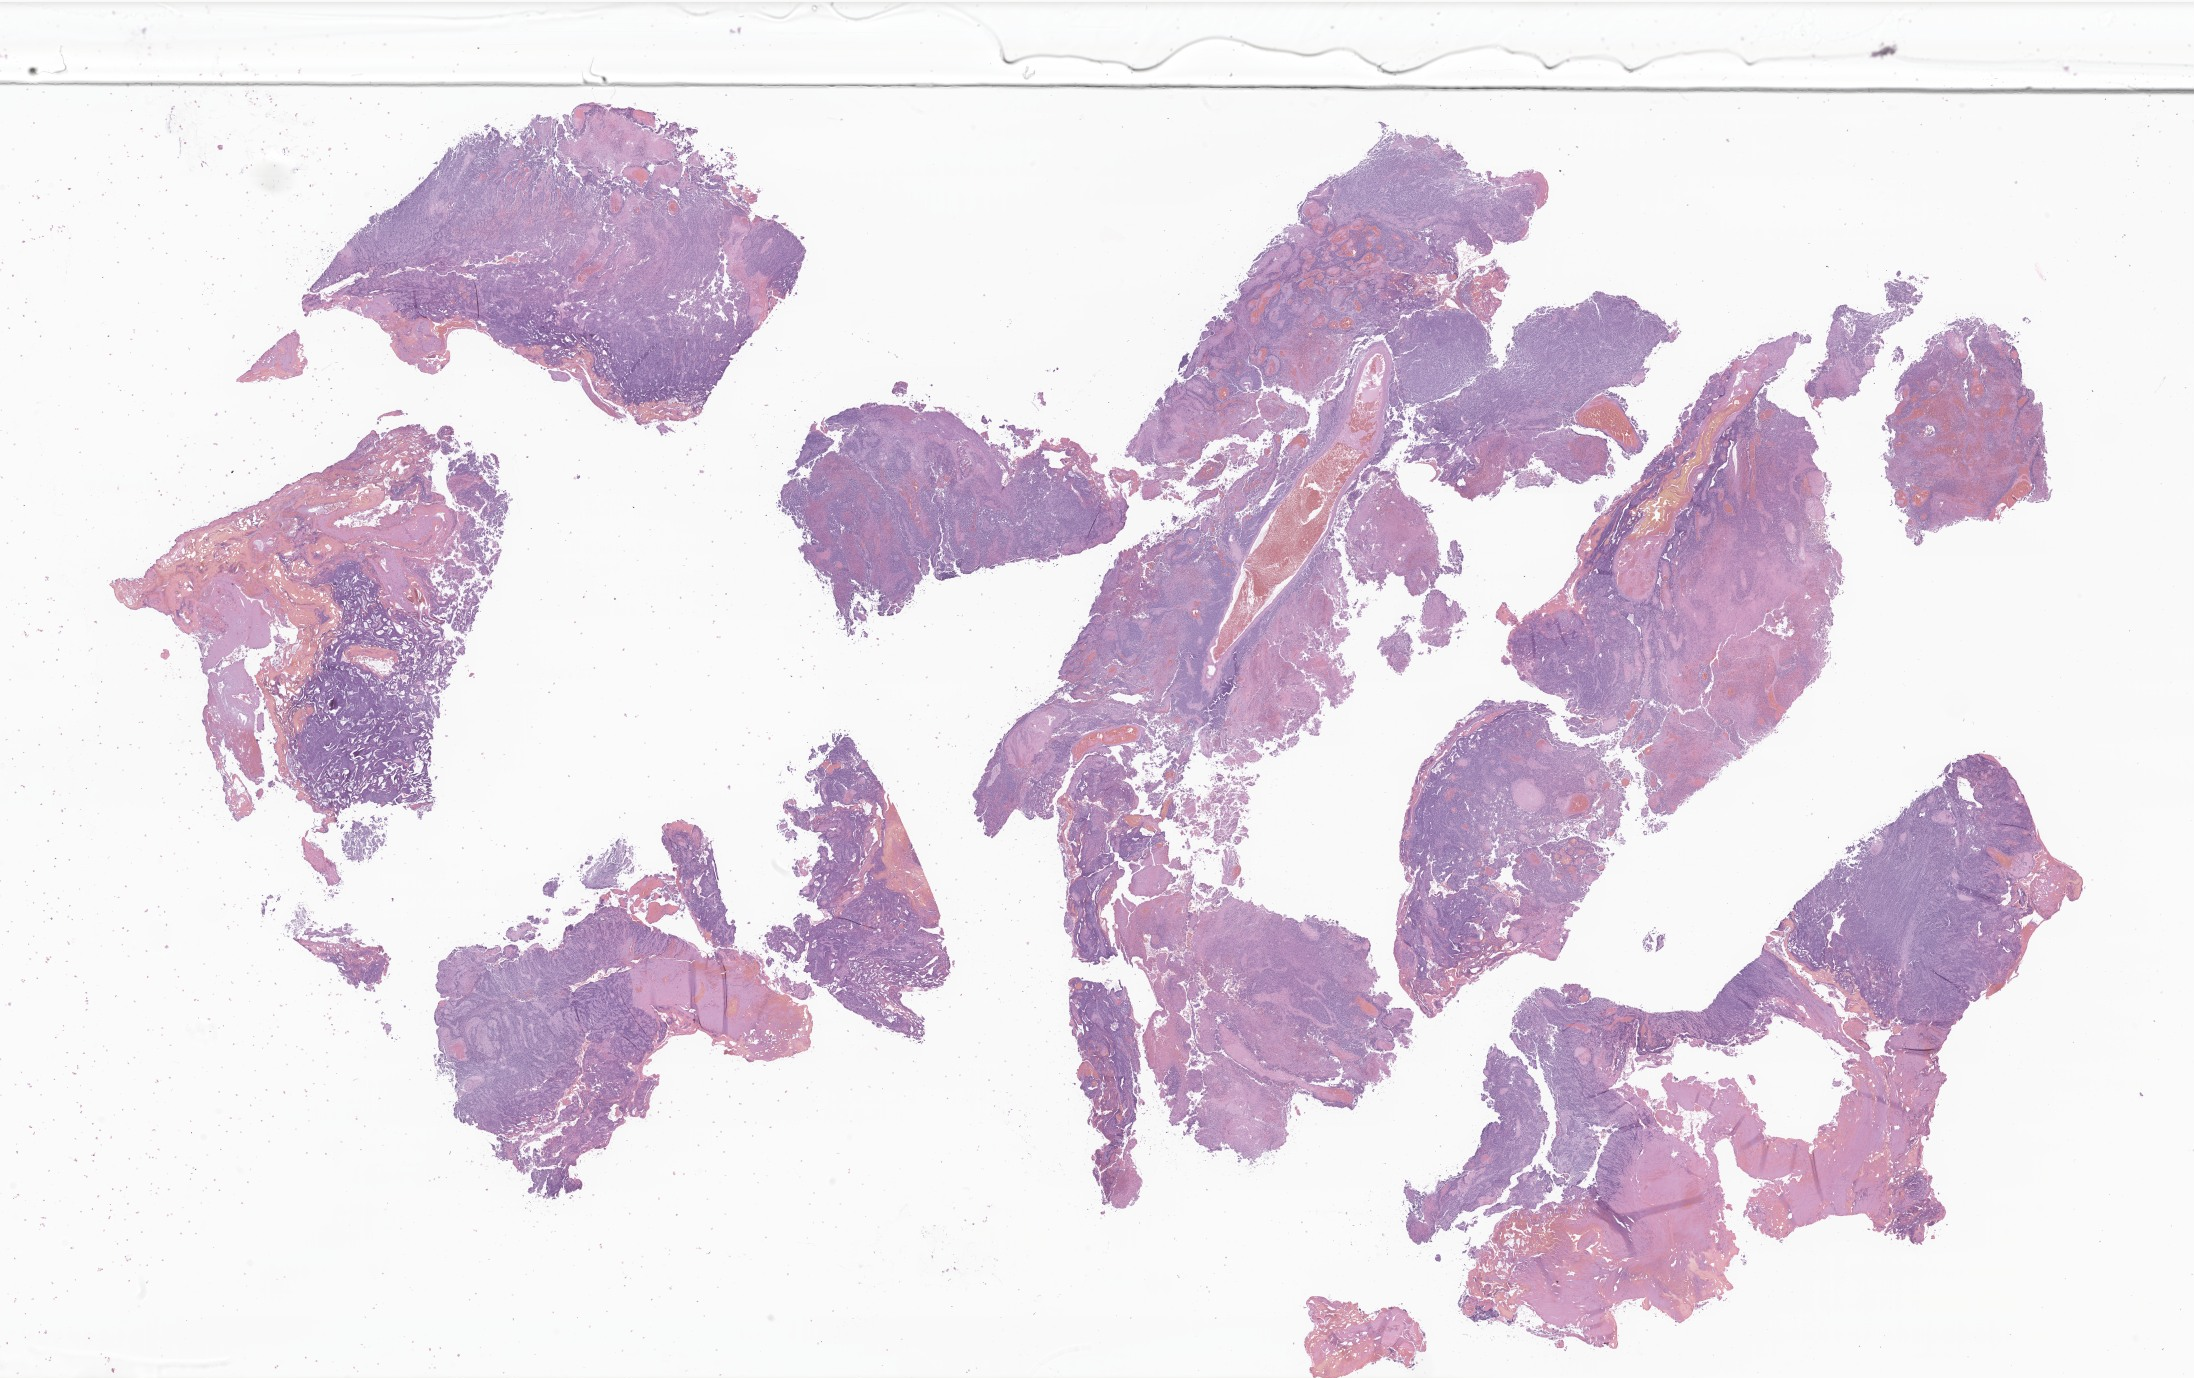
Whole-slide image, H&E stain of tumor tissue from the cerebellum, whole scanned area (about 37.0 x 23.2 mm) shown as a low-resolution overview, formalin-fixed, paraffin-embedded (FFPE) tissue. Patient: male, age 60 months (5 years).
Recorded diagnosis: Medulloblastoma, NOS.